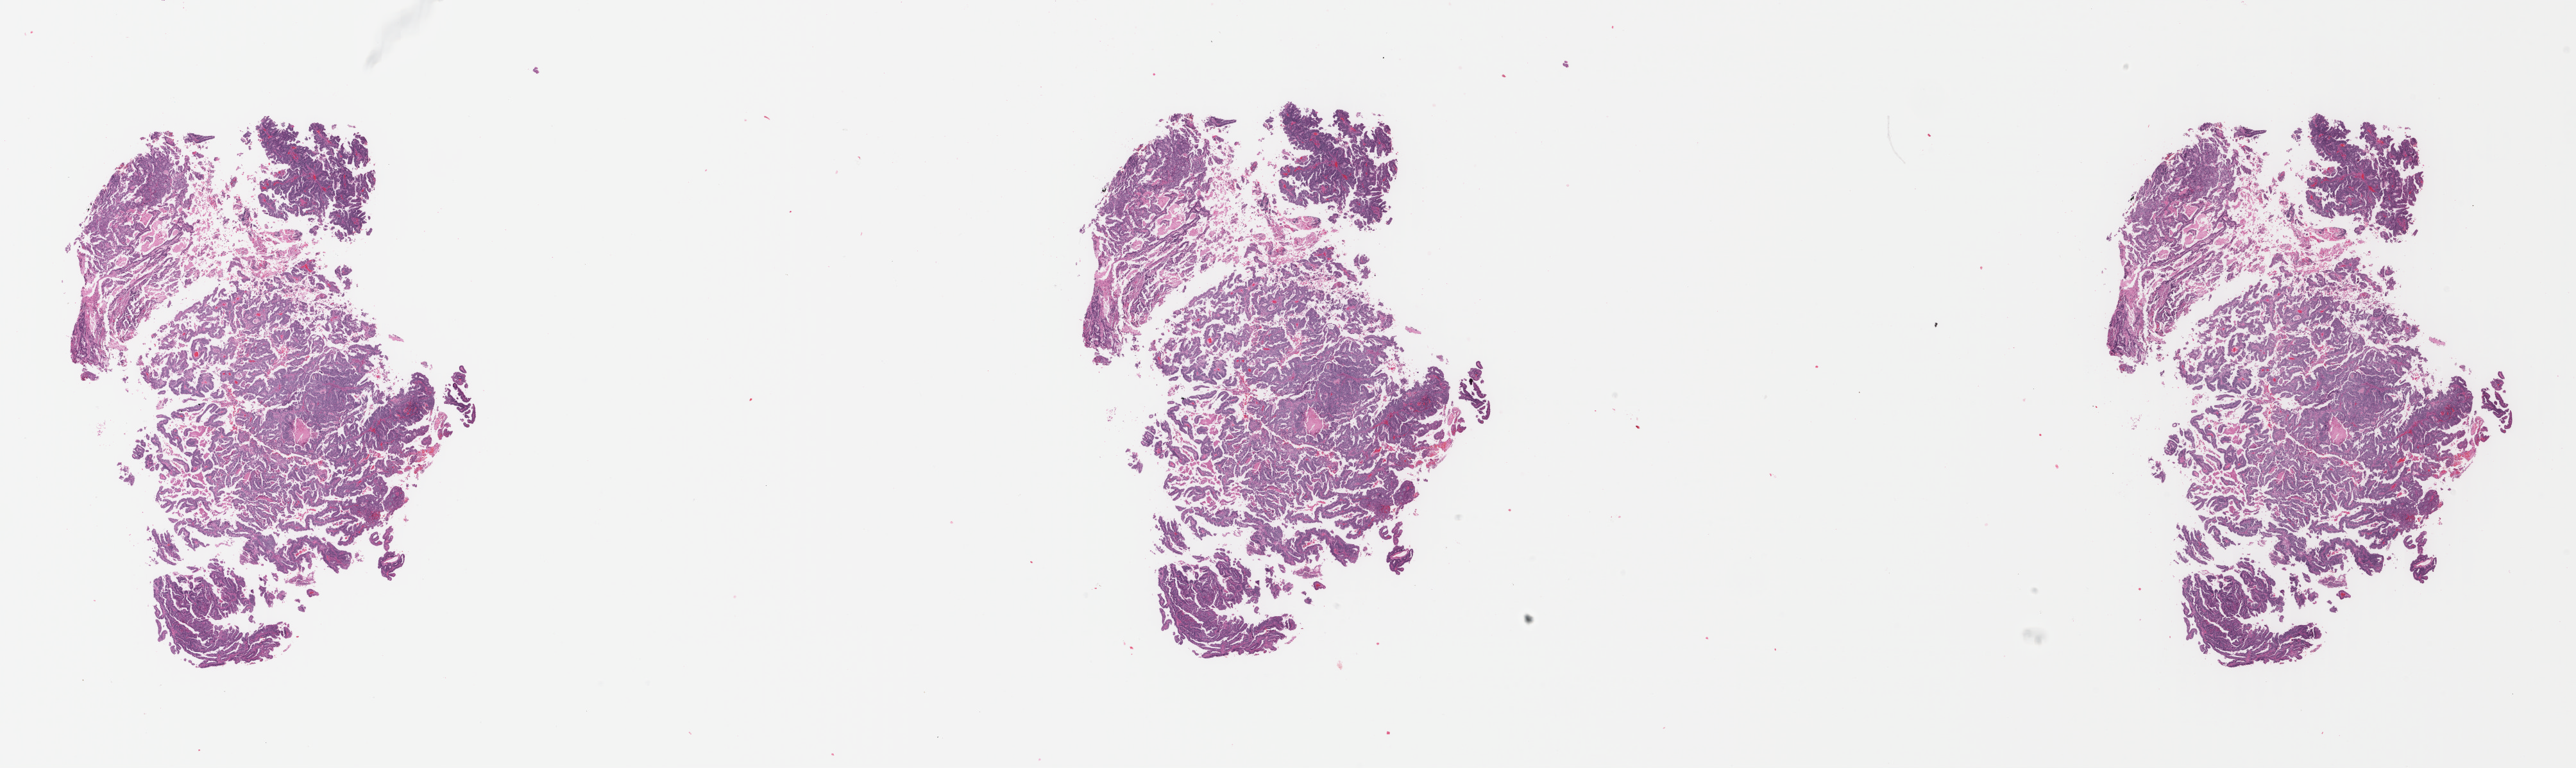
Digitized H&E-stained tissue section (whole slide) — low-resolution overview of the scanned area, about 31.9 x 9.5 mm, formalin-fixed paraffin-embedded (FFPE) diagnostic section, uterus, primary tumour sample. Patient: female, age at initial diagnosis 86 years. Histologic grade: G2 (moderately differentiated).
• histologic diagnosis: Endometrioid adenocarcinoma, NOS (endometrium)
• FIGO stage: II